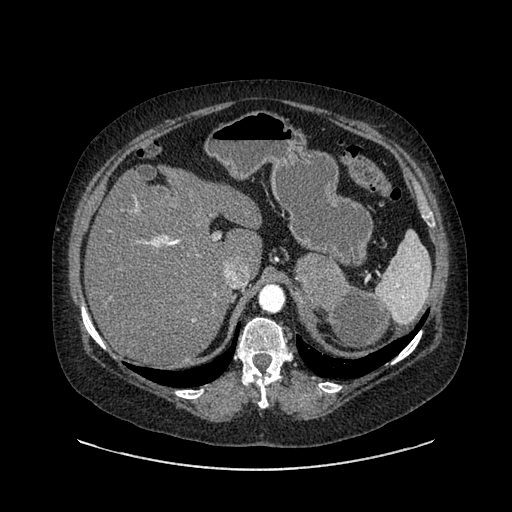
Contrast-enhanced abdominal CT, one axial slice; position 616 of 769 along the scan axis; 120 kVp; intravenous contrast given; soft-tissue window (W 400 / L 40 HU); 512 × 512 image matrix, field of view 460 × 460 mm. Patient: female, 61 years. Case-level facts recorded for this patient, not image findings: diagnosis: adrenocortical carcinoma; tumour side: left adrenal; tumour size at pathology: 13 cm; Ki-67 index: 79 %; stage (as recorded): 2.
Outlined on this slice (semi-automatically segmented with operator editing):
- mass: bounding box <296,255,389,350> (left, top, right, bottom; pixels)